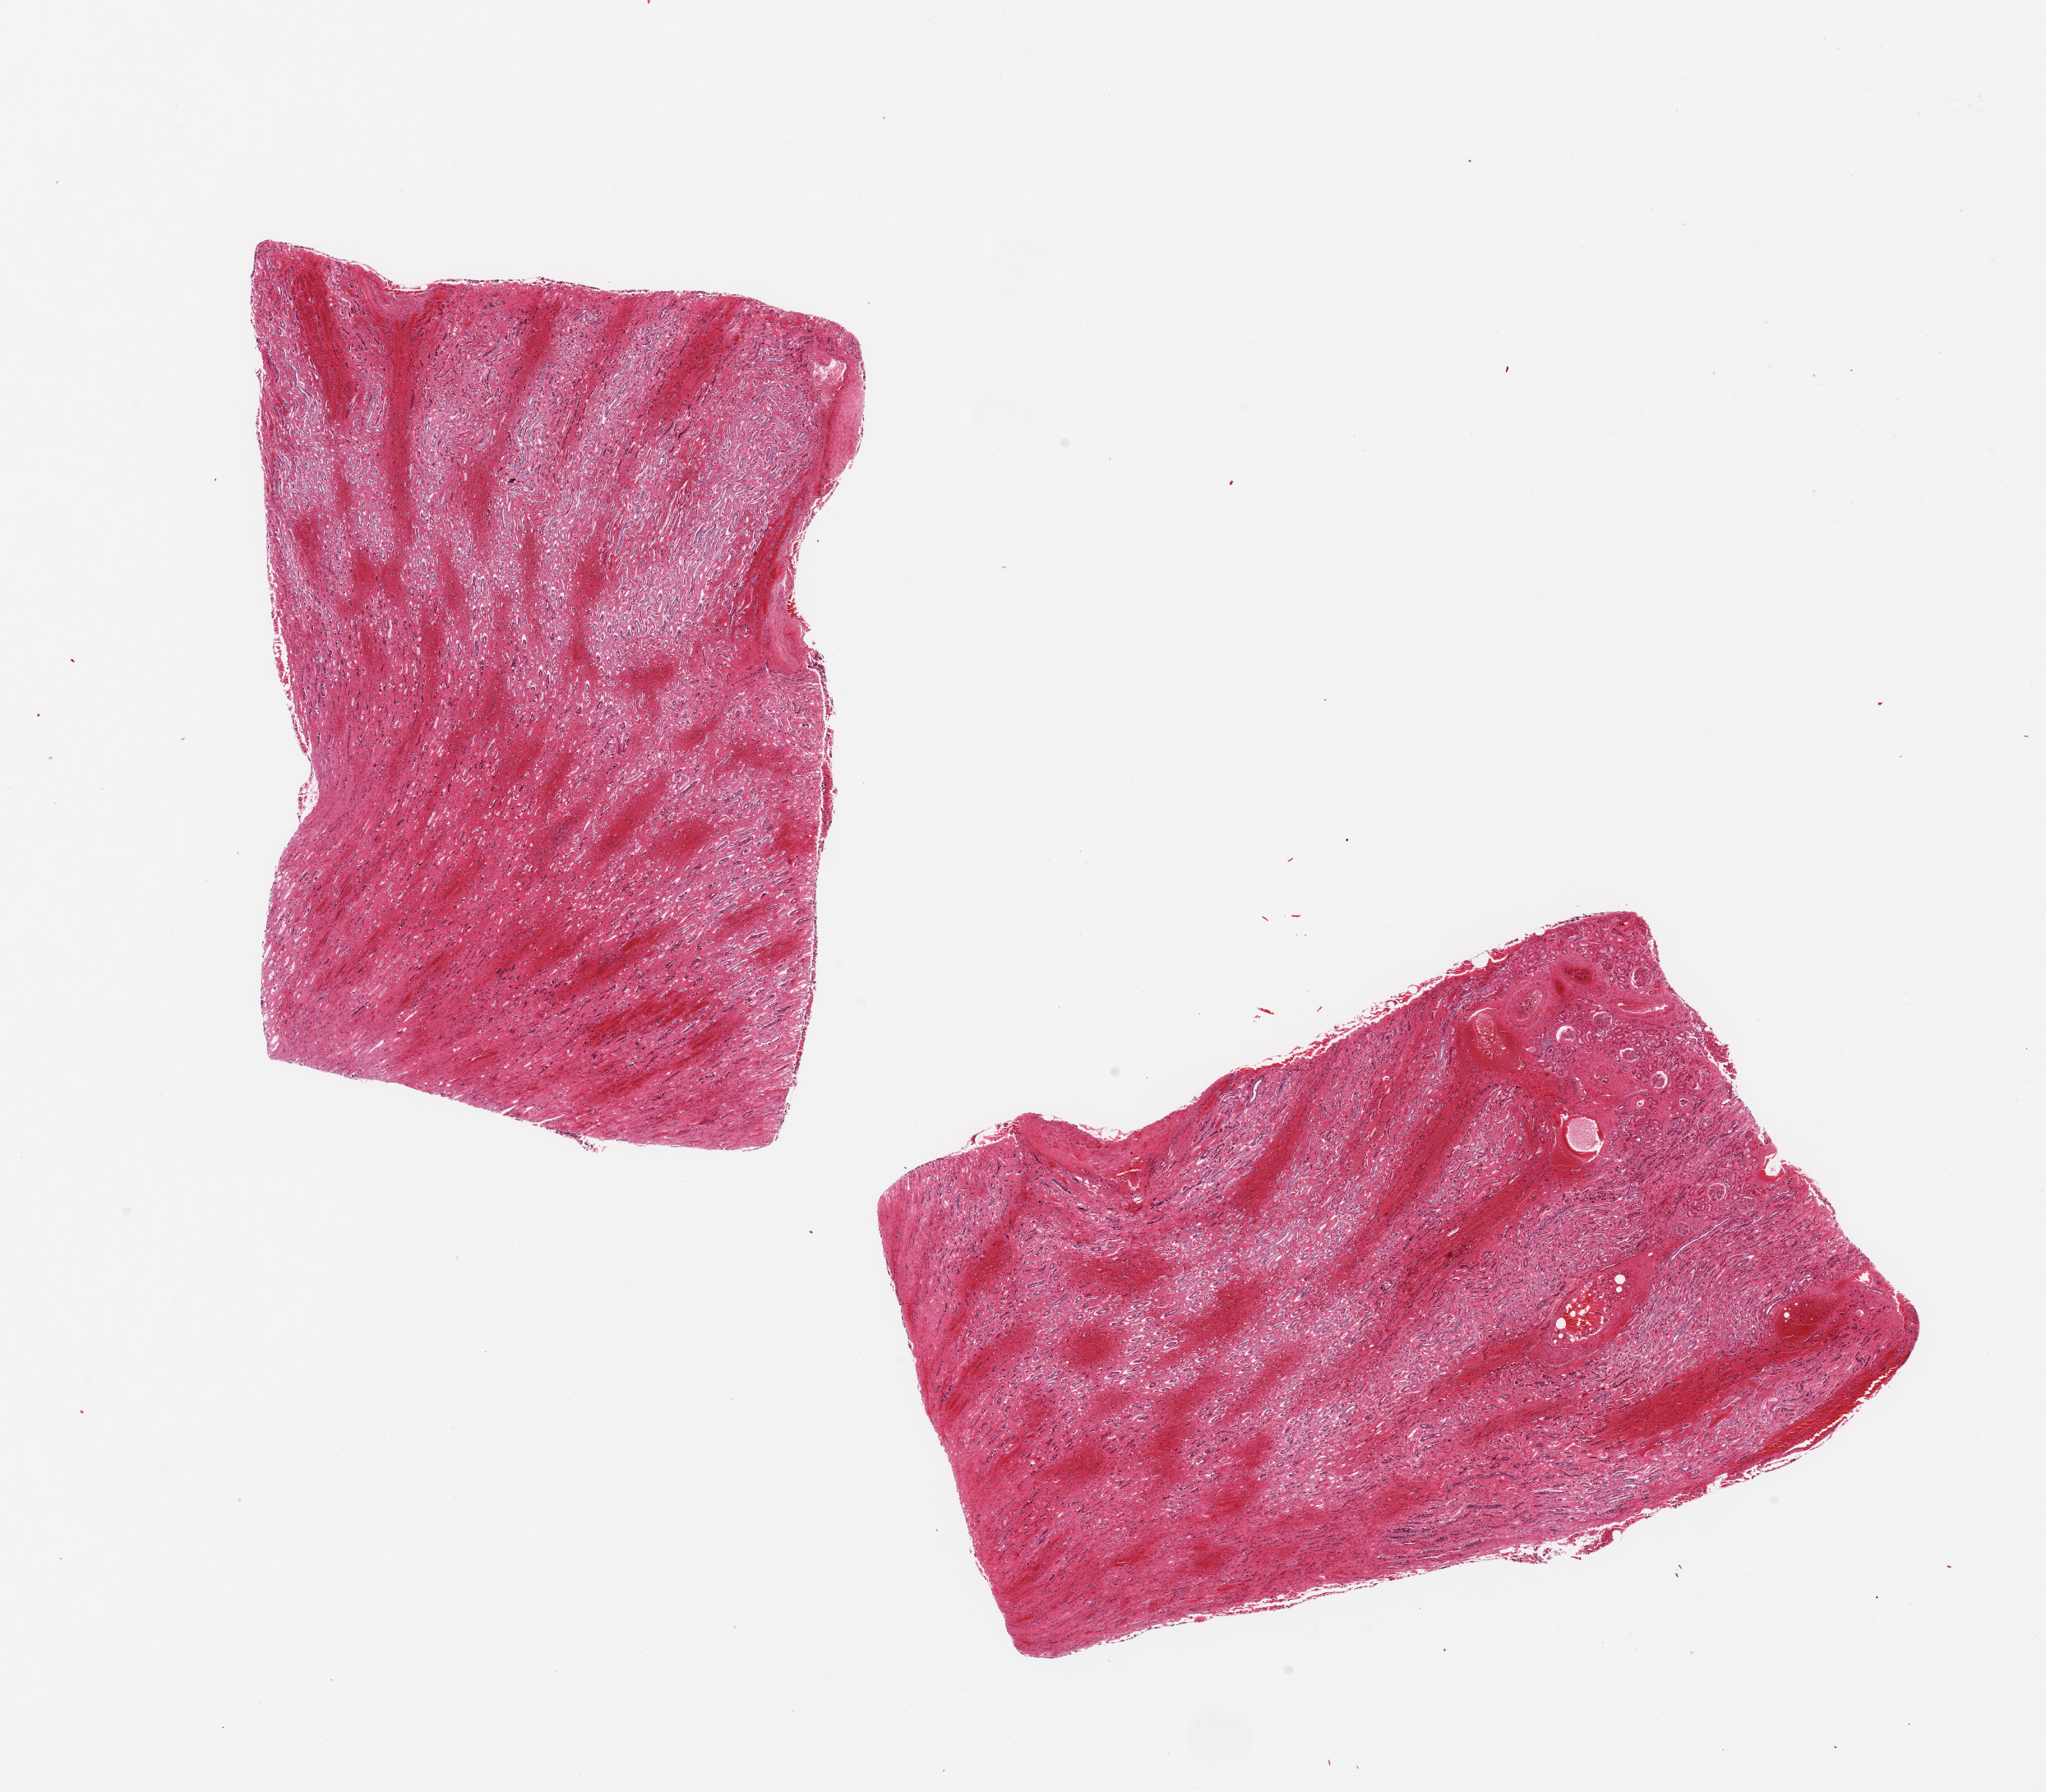
Digitized haematoxylin and eosin-stained section — low-resolution overview of the scanned area, about 19.7 x 17.2 mm. PAXgene-fixed paraffin-embedded (PFPE) section. Target tissue: renal medulla. Donor tissue sample. Donor: male.
- pathologist's review note for this sample: 2 pieces ~9x5mm, one has ~10% cortex 'contamination'